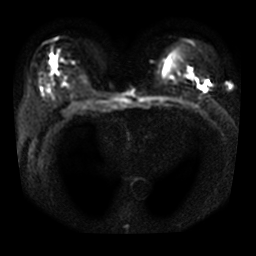
Breast MRI, one axial slice; slice 19 of 33 in the series (ordered by position); diffusion-weighted series; image 2 of 4 stored at this slice position (different b-values; order by instance number); 3 T; 256 × 256 image matrix, field of view 320 × 320 mm. Female patient.
Structures marked on this image (expert manual segmentation):
- tumour on diffusion-weighted imaging: box from (x=205, y=82) to (x=210, y=86) px